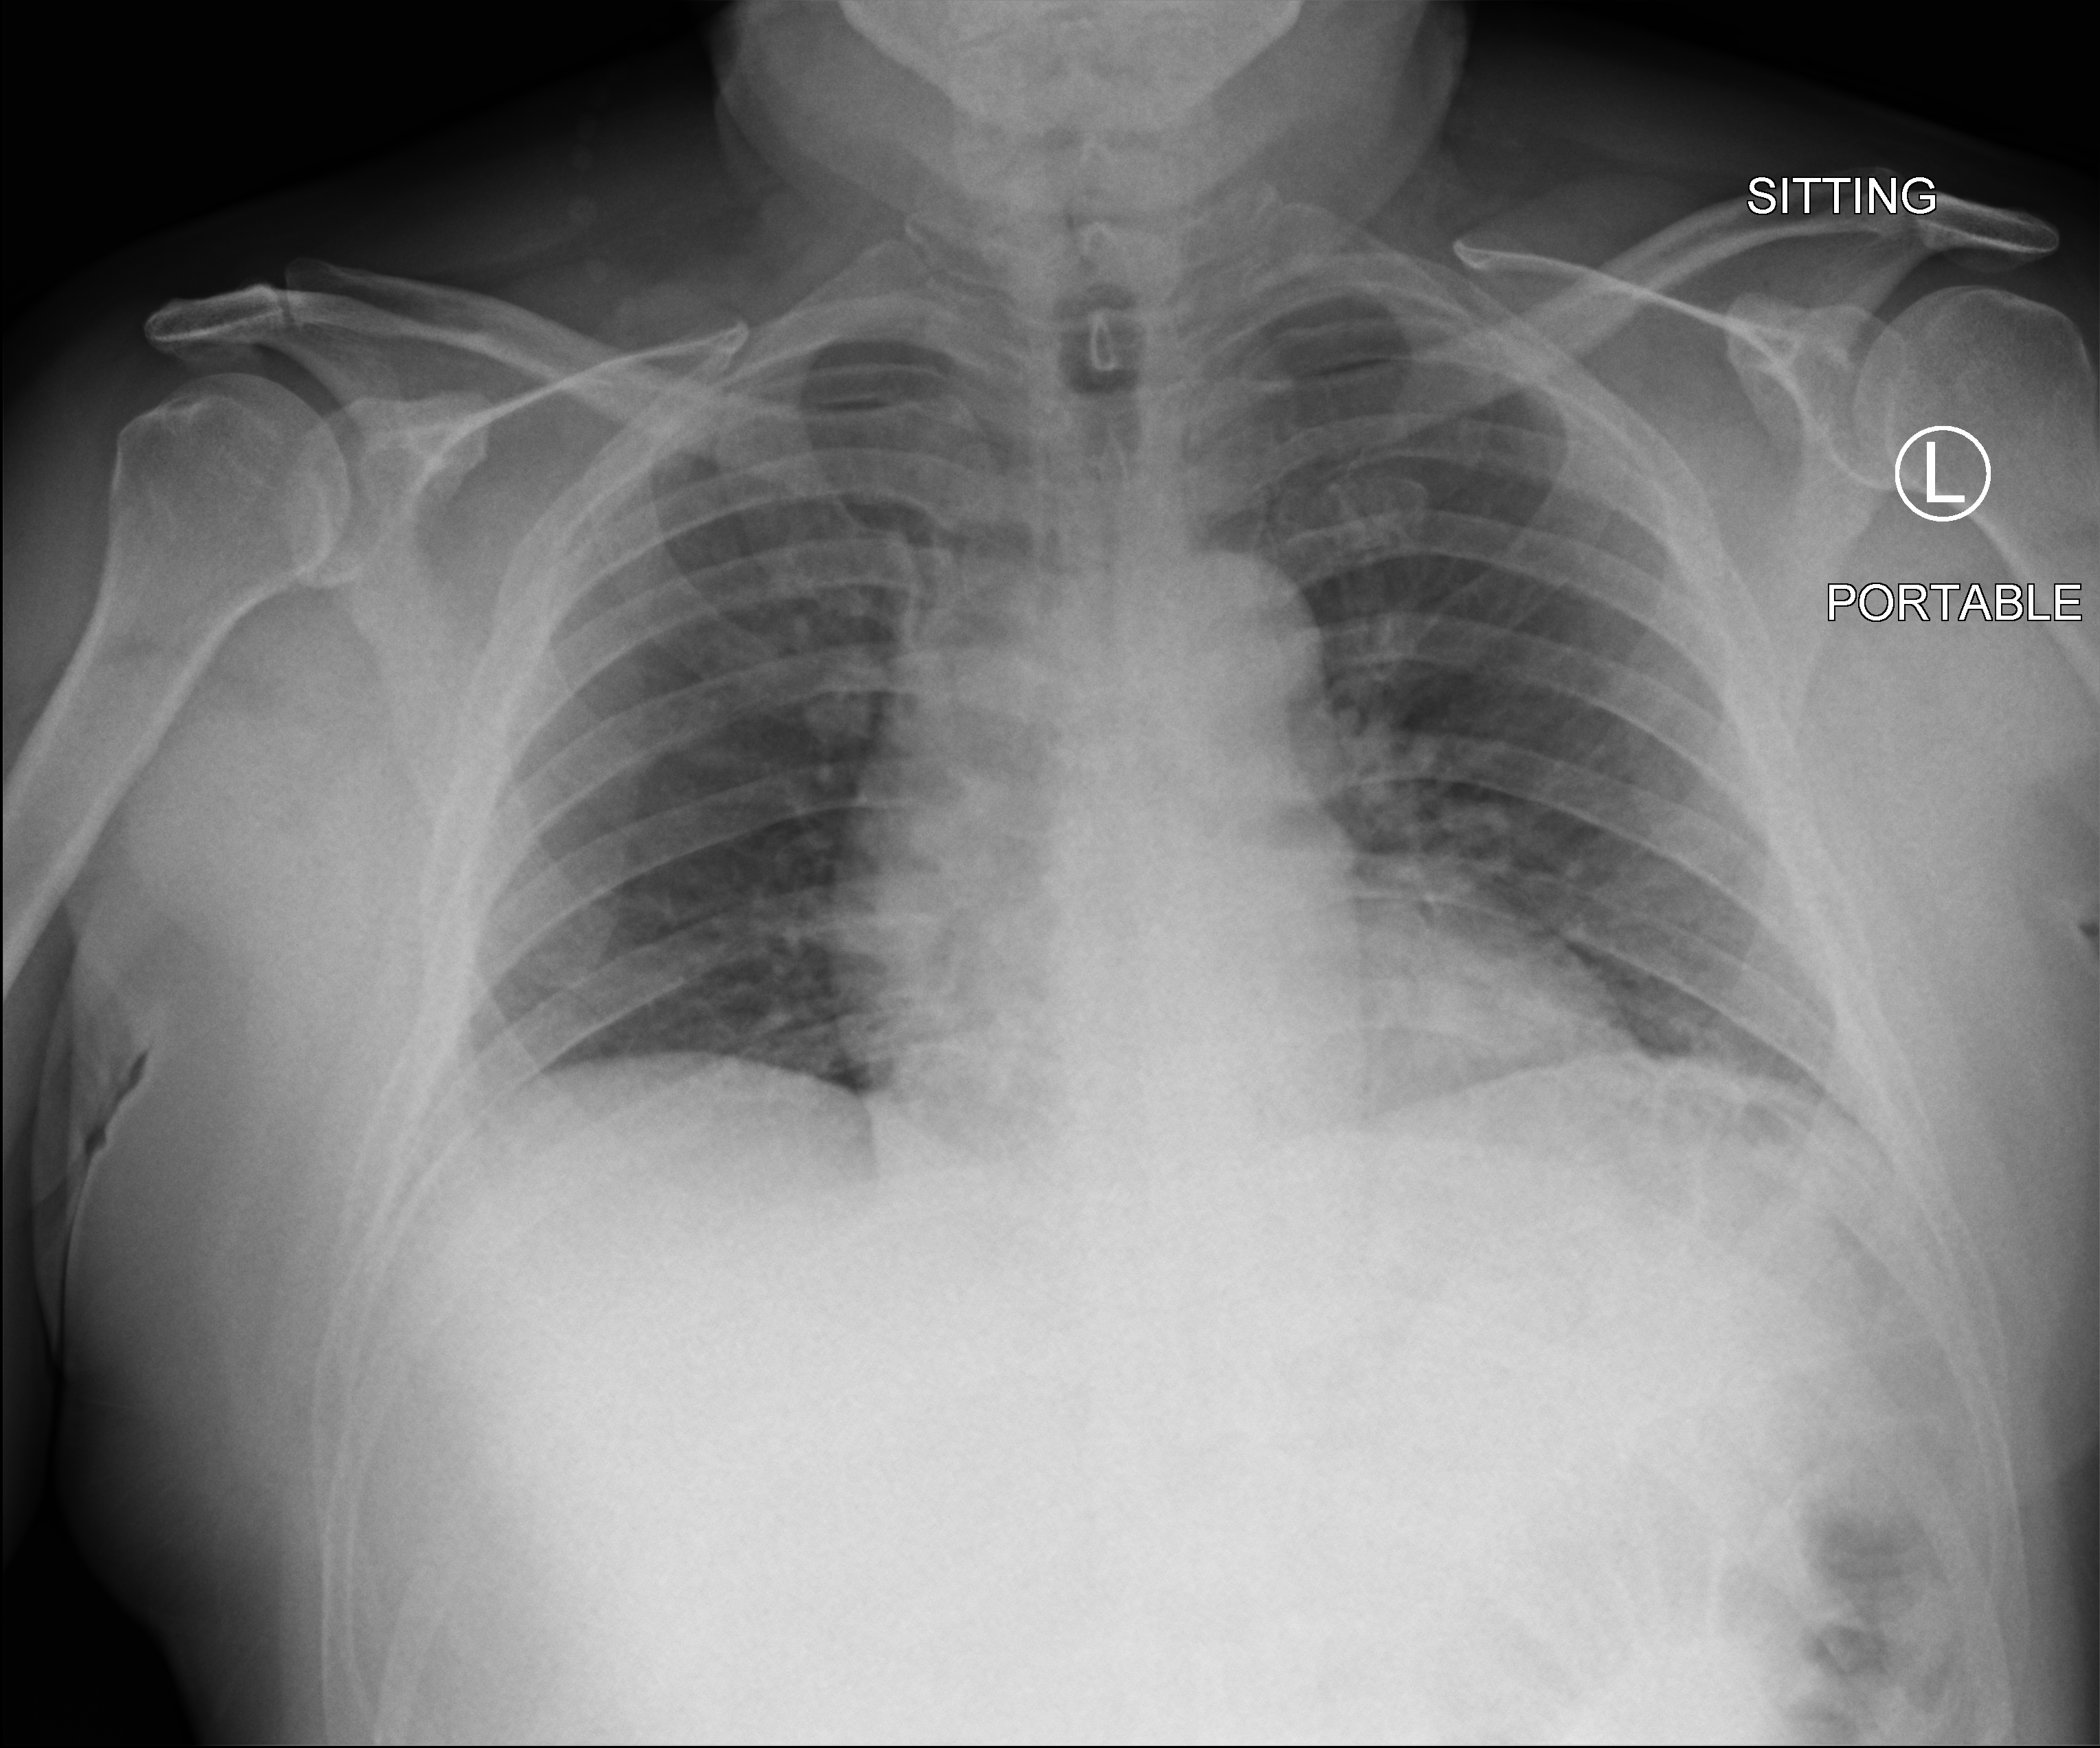
Chest X-ray (portable), anteroposterior (AP) projection. Male patient hospitalised with COVID-19, age 60–74 years.
From the hospital-stay record, not from the radiograph (when in the stay this image was taken is not recorded):
- admitted to intensive care during this hospital stay: no
- mechanically ventilated during this hospital stay: no
- length of hospital stay: 1 day